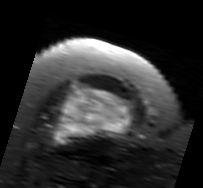
MRI of an extremity soft-tissue mass, one axial slice; slice 60 of 91 in the series (ordered by position); T2-weighted fat-saturated; MR volume resampled by the dataset authors to the PET/CT grid (not the native acquisition matrix); 203 × 188 image matrix, field of view 198 × 184 mm. Female patient. From the clinical record (not read from this slice): histological type: malignant solitary fibrous tumor; grade: intermediate; site of the primary tumour: right thigh.
Outlined on this slice (expert contour drawn on MRI and transferred to this co-registered scan by the dataset authors):
- gross tumour volume including surrounding oedema: box from (x=51, y=83) to (x=132, y=148) px
- gross tumour volume (mass): (x=53, y=86)–(x=132, y=146)